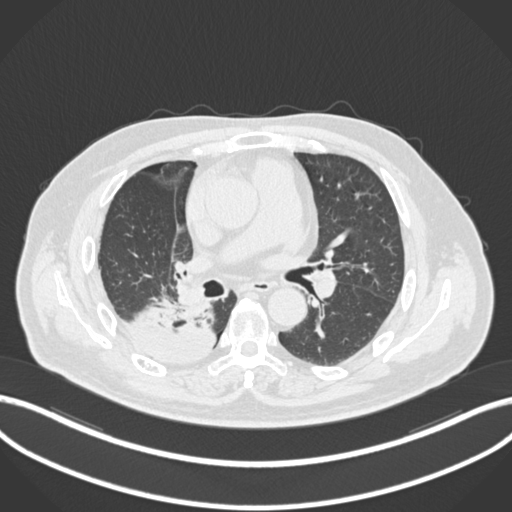
Chest CT, one axial slice. Slice 101 of 218 in the series (ordered by position). 120 kVp. Lung window (W 1500 / L -600 HU). 512 × 512 image matrix, field of view 400 × 400 mm. Patient: male, 68 years. From the clinical record (not read from this slice): clinical TNM (as recorded): T2a N0 M0.
Annotated regions visible in this slice (rectangle marked by the reading radiologist):
- lung tumour (recorded histology: adenocarcinoma): bounding box <122,293,215,365> (left, top, right, bottom; pixels)